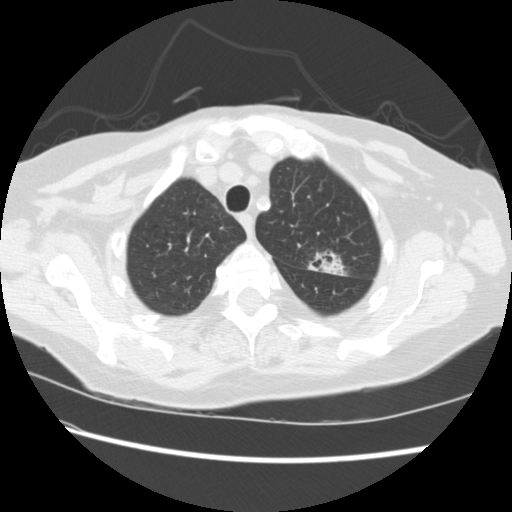
Low-dose screening chest CT, axial slice. First (baseline) screen. Lung window (W 1500 / L -600 HU). 2.5 mm slice thickness. 512 × 512 image matrix. Female, age 74 years at enrolment. Former smoker at enrolment.
Lesion marked by an expert reader, bounding box (x1, y1, x2, y2) in pixels: (297, 243, 347, 283). The screening reader recorded 2 non-calcified nodules or masses ≥4 mm on this exam (left upper lobe, right lower lobe); which of them this box marks is not recorded. Lung cancer was diagnosed 309 days after this screen: non-small cell carcinoma, left upper lobe, stage IV (AJCC 6th edition).